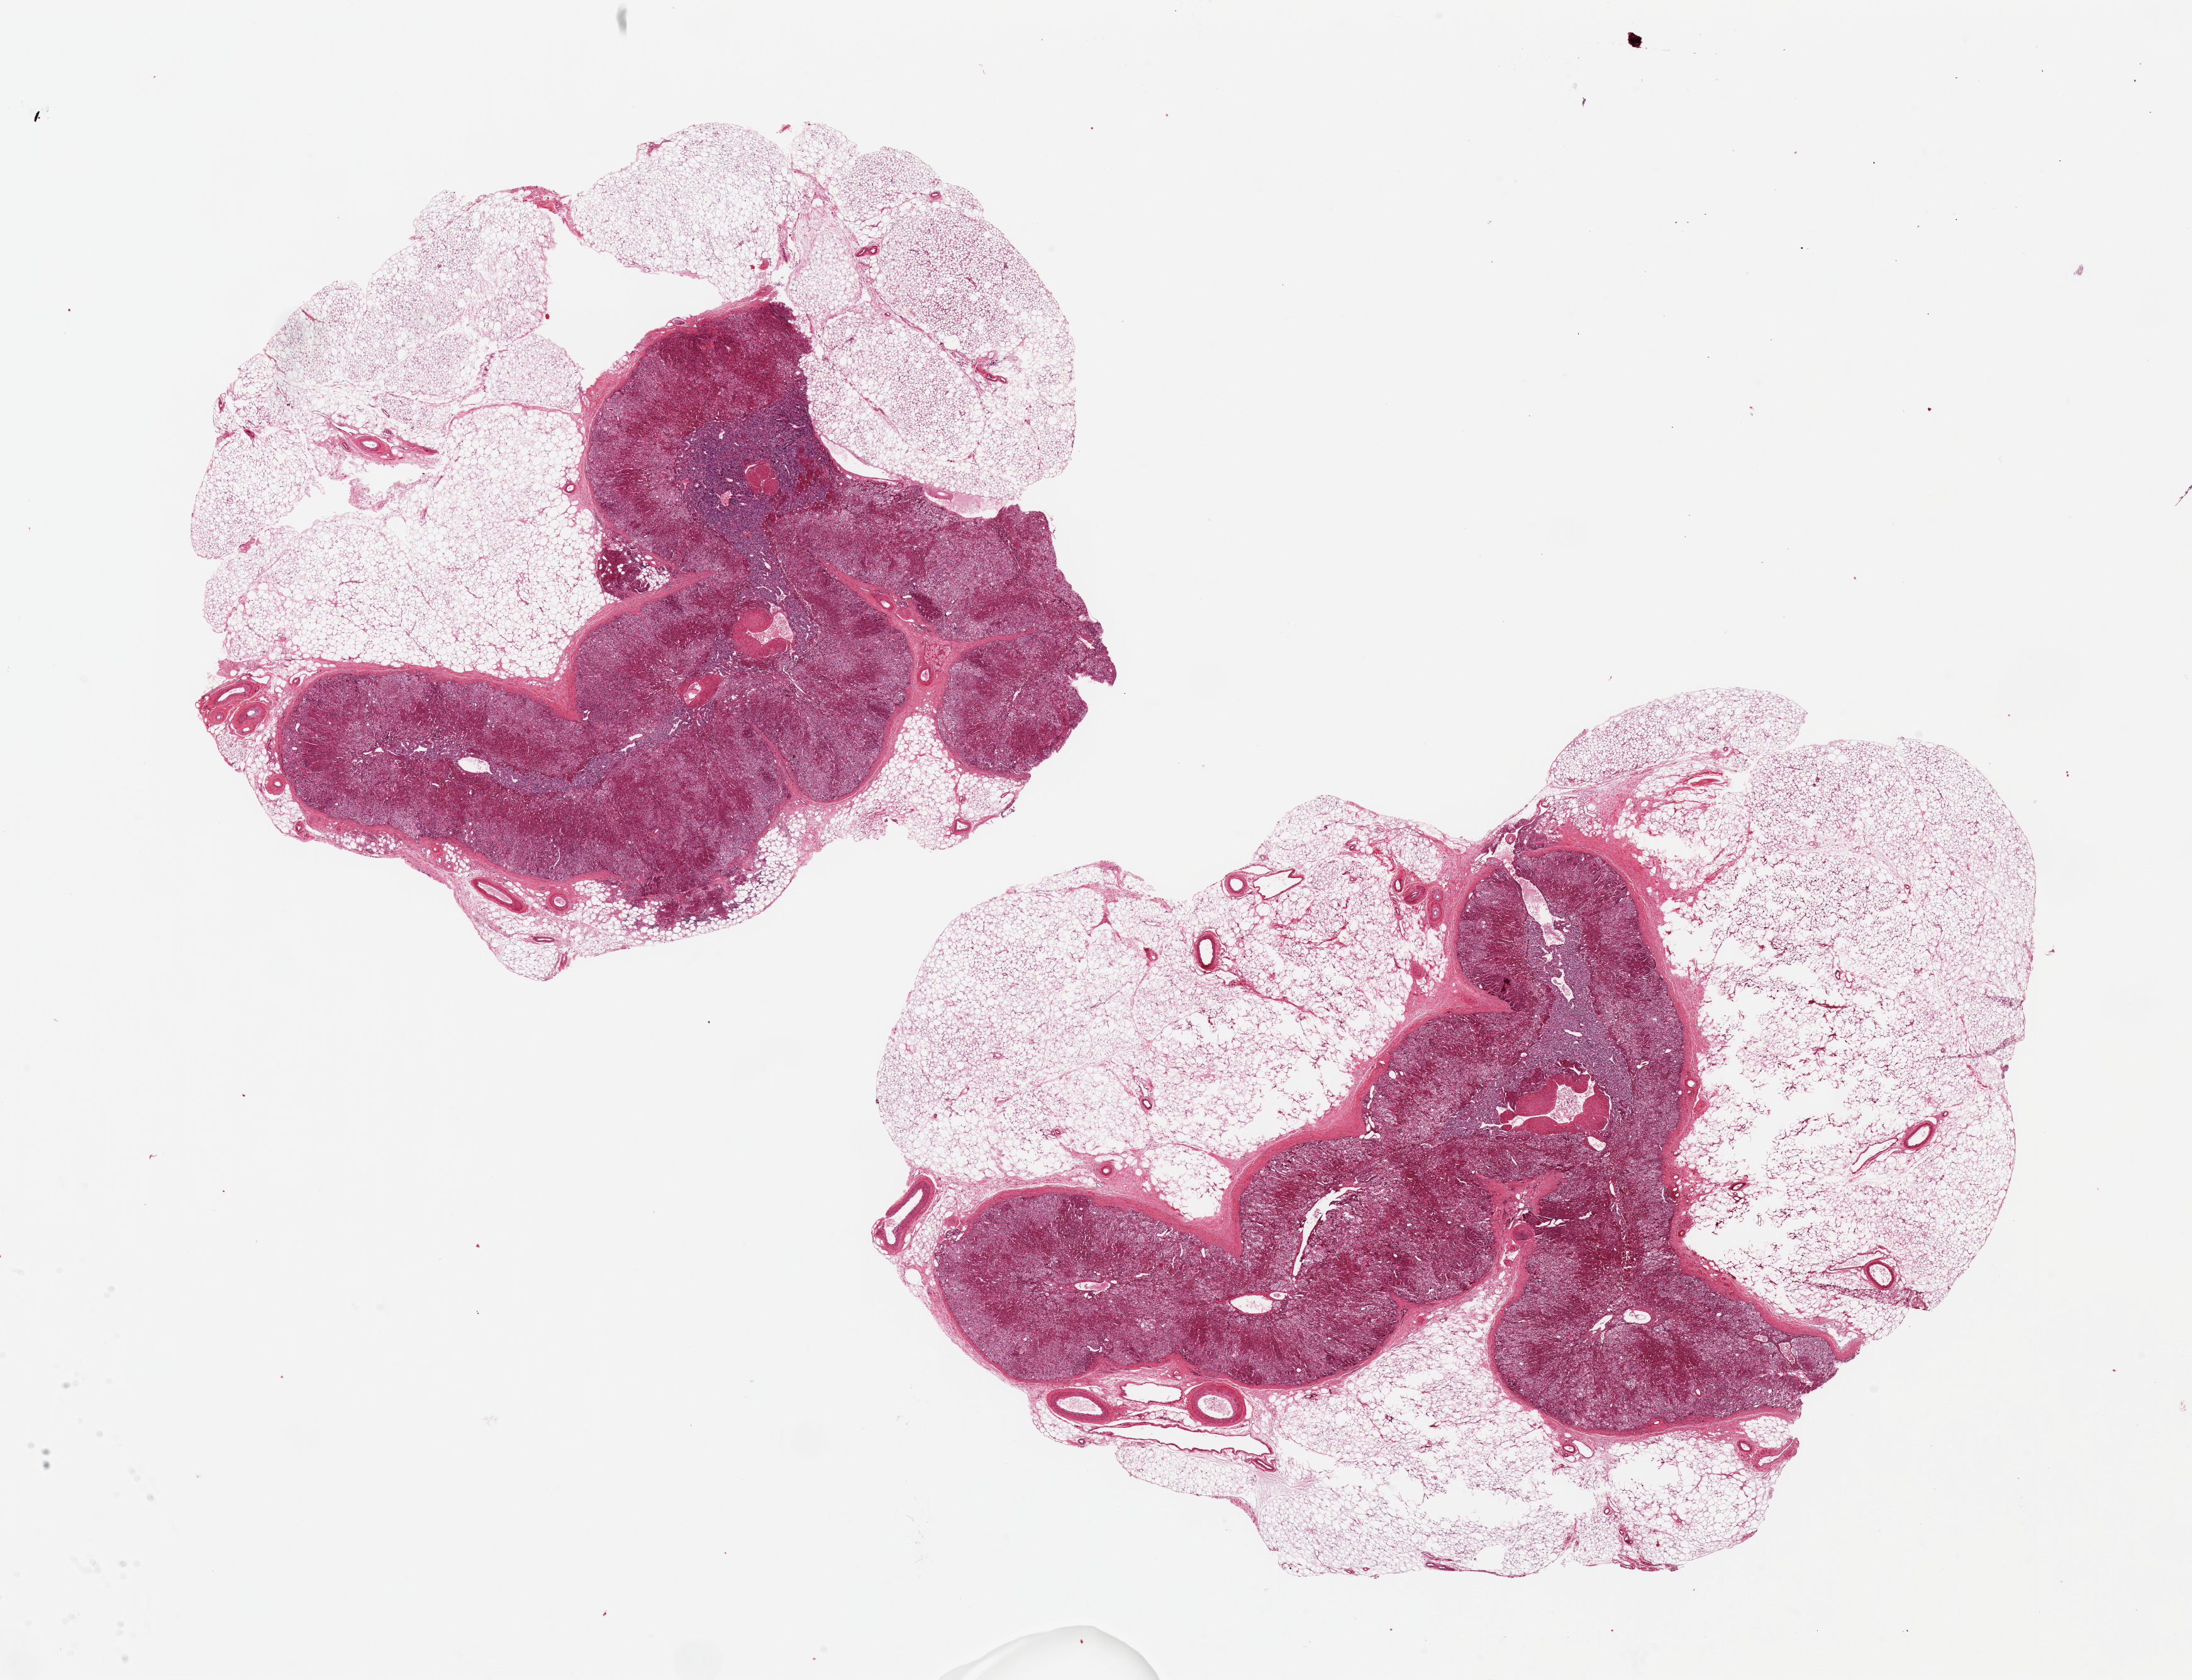
Hematoxylin and eosin (H&E) whole-slide image, brightfield, shown as a low-resolution overview of the whole scanned area (about 27.6 x 21.1 mm, slide scanned at 20x), PAXgene-fixed paraffin-embedded (PFPE) section, target tissue: adrenal gland, donor tissue sample. Male donor.
Review note (as recorded): 2 pieces ~11x6mm, well preserved; promient medulla presentp to 2mm d., and in both; Abundant adherent fat up to ~3mm on both.